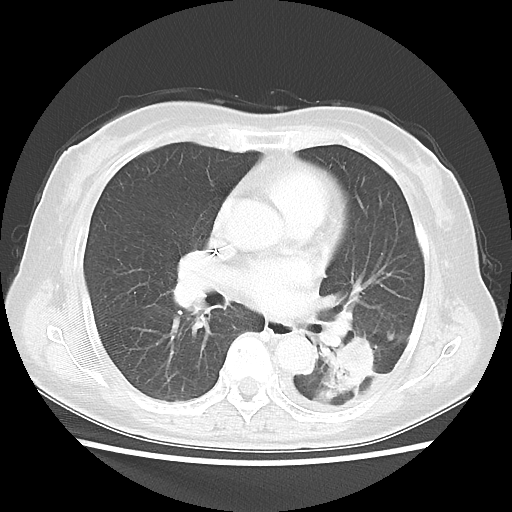
Chest CT, one axial slice; position 19 of 40 along the scan axis; lung window (W 1500 / L -600 HU); 5 mm slice thickness; 512 × 512 image matrix, field of view 341 × 341 mm. Patient: female, 69 years. Case-level facts recorded for this patient, not image findings: clinical TNM (as recorded): T1c N0 M0.
Structures marked on this image (rectangle marked by the reading radiologist):
- lung tumour (recorded histology: adenocarcinoma): box from (x=323, y=327) to (x=379, y=398) px